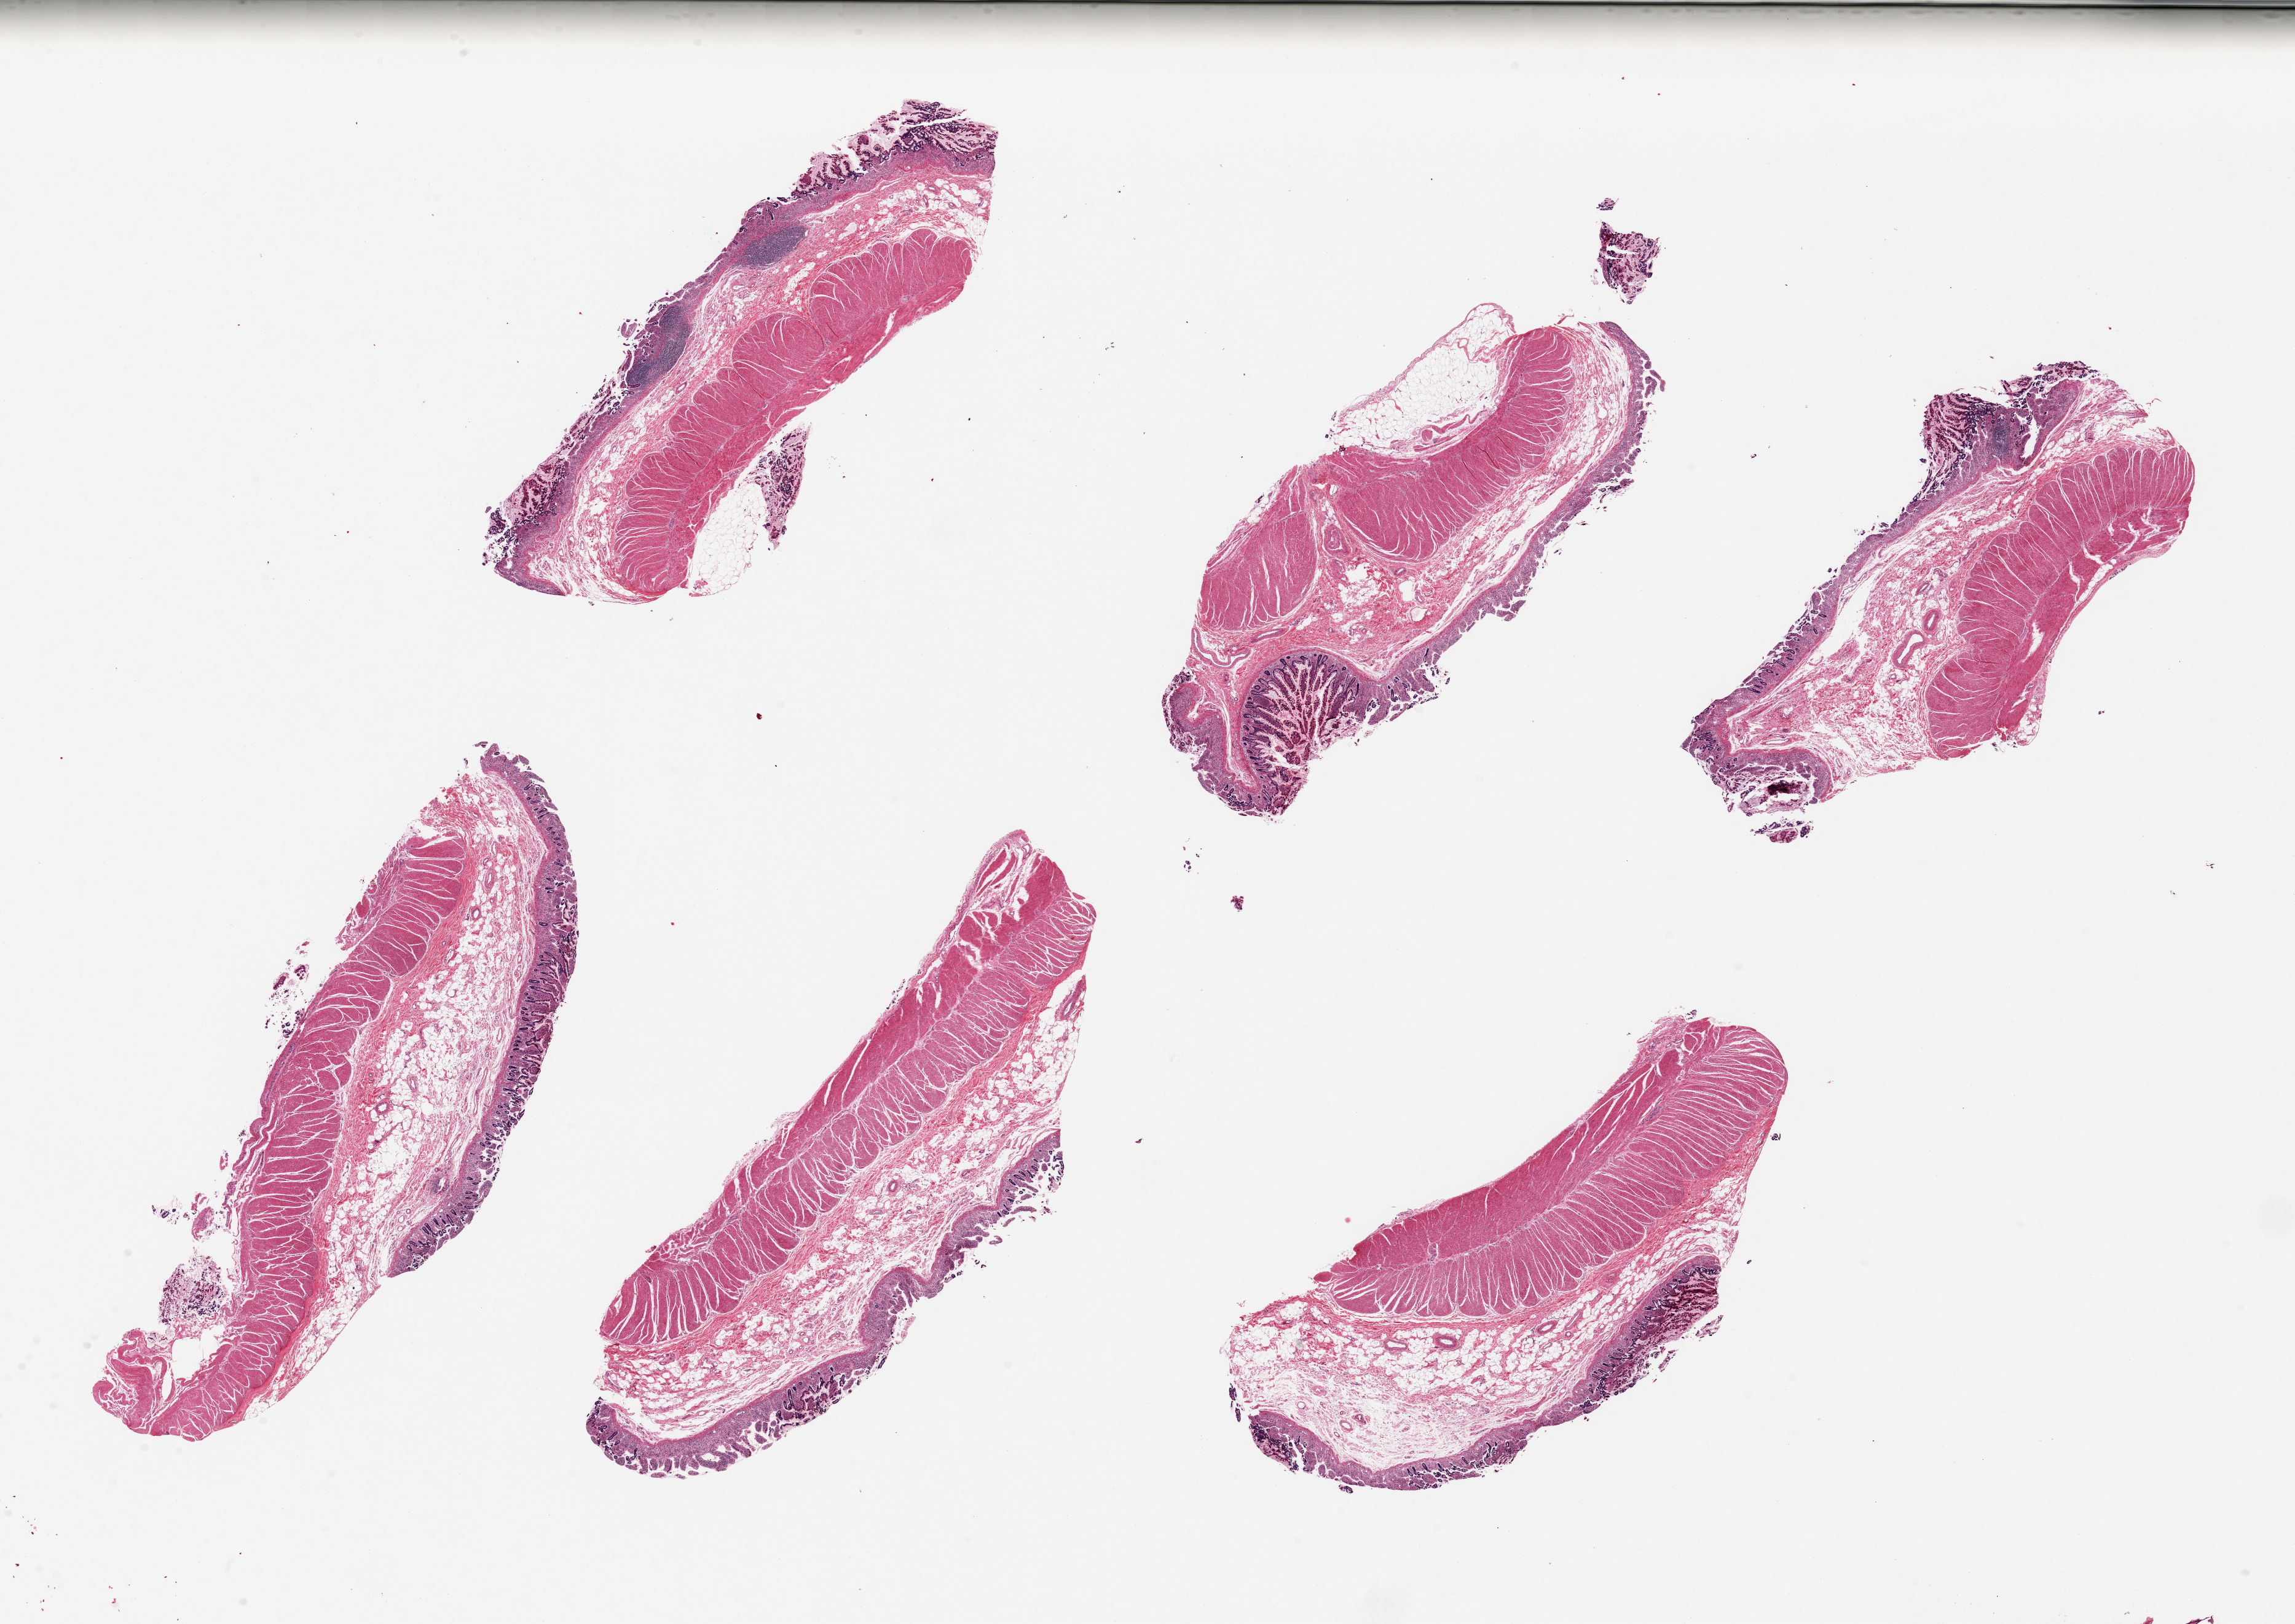
Digitized haematoxylin and eosin-stained section — low-resolution overview of the scanned area, about 29.5 x 20.9 mm; PAXgene-fixed paraffin-embedded (PFPE) section; target tissue: ileum; tissue donor sample. Male donor.
Review note (as recorded): 6 pieces ~8x3mm; Includes all layers, autolyzed mucosa, rare germinal centers.